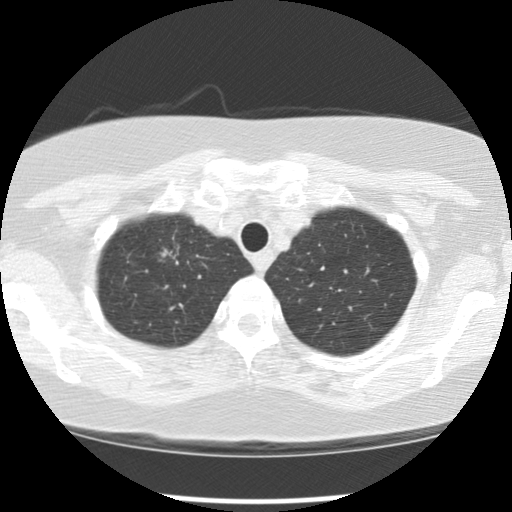
Chest CT (low-dose screening protocol), one axial image, baseline screening round, lung window (W 1500 / L -600 HU), 2.5 mm slice thickness, standard (soft-tissue) reconstruction kernel (STANDARD), slice 16 of 113 in the series. Female, age 65 years at enrolment. Current smoker at enrolment.
Expert reader's lesion annotation, box from (x=148, y=232) to (x=196, y=280) px. The screening reader recorded 2 non-calcified nodules or masses ≥4 mm on this exam; which of them this box marks is not recorded. Official screen result: positive, change unspecified: nodule(s) >= 4 mm or enlarging nodule(s), mass(es), or other non-specific abnormalities suspicious for lung cancer. Participant outcome: lung cancer diagnosed 183 days after this screen — large cell carcinoma, NOS, right upper lobe, poorly differentiated (G3), stage IA (AJCC 6th edition), 20 mm at pathology.